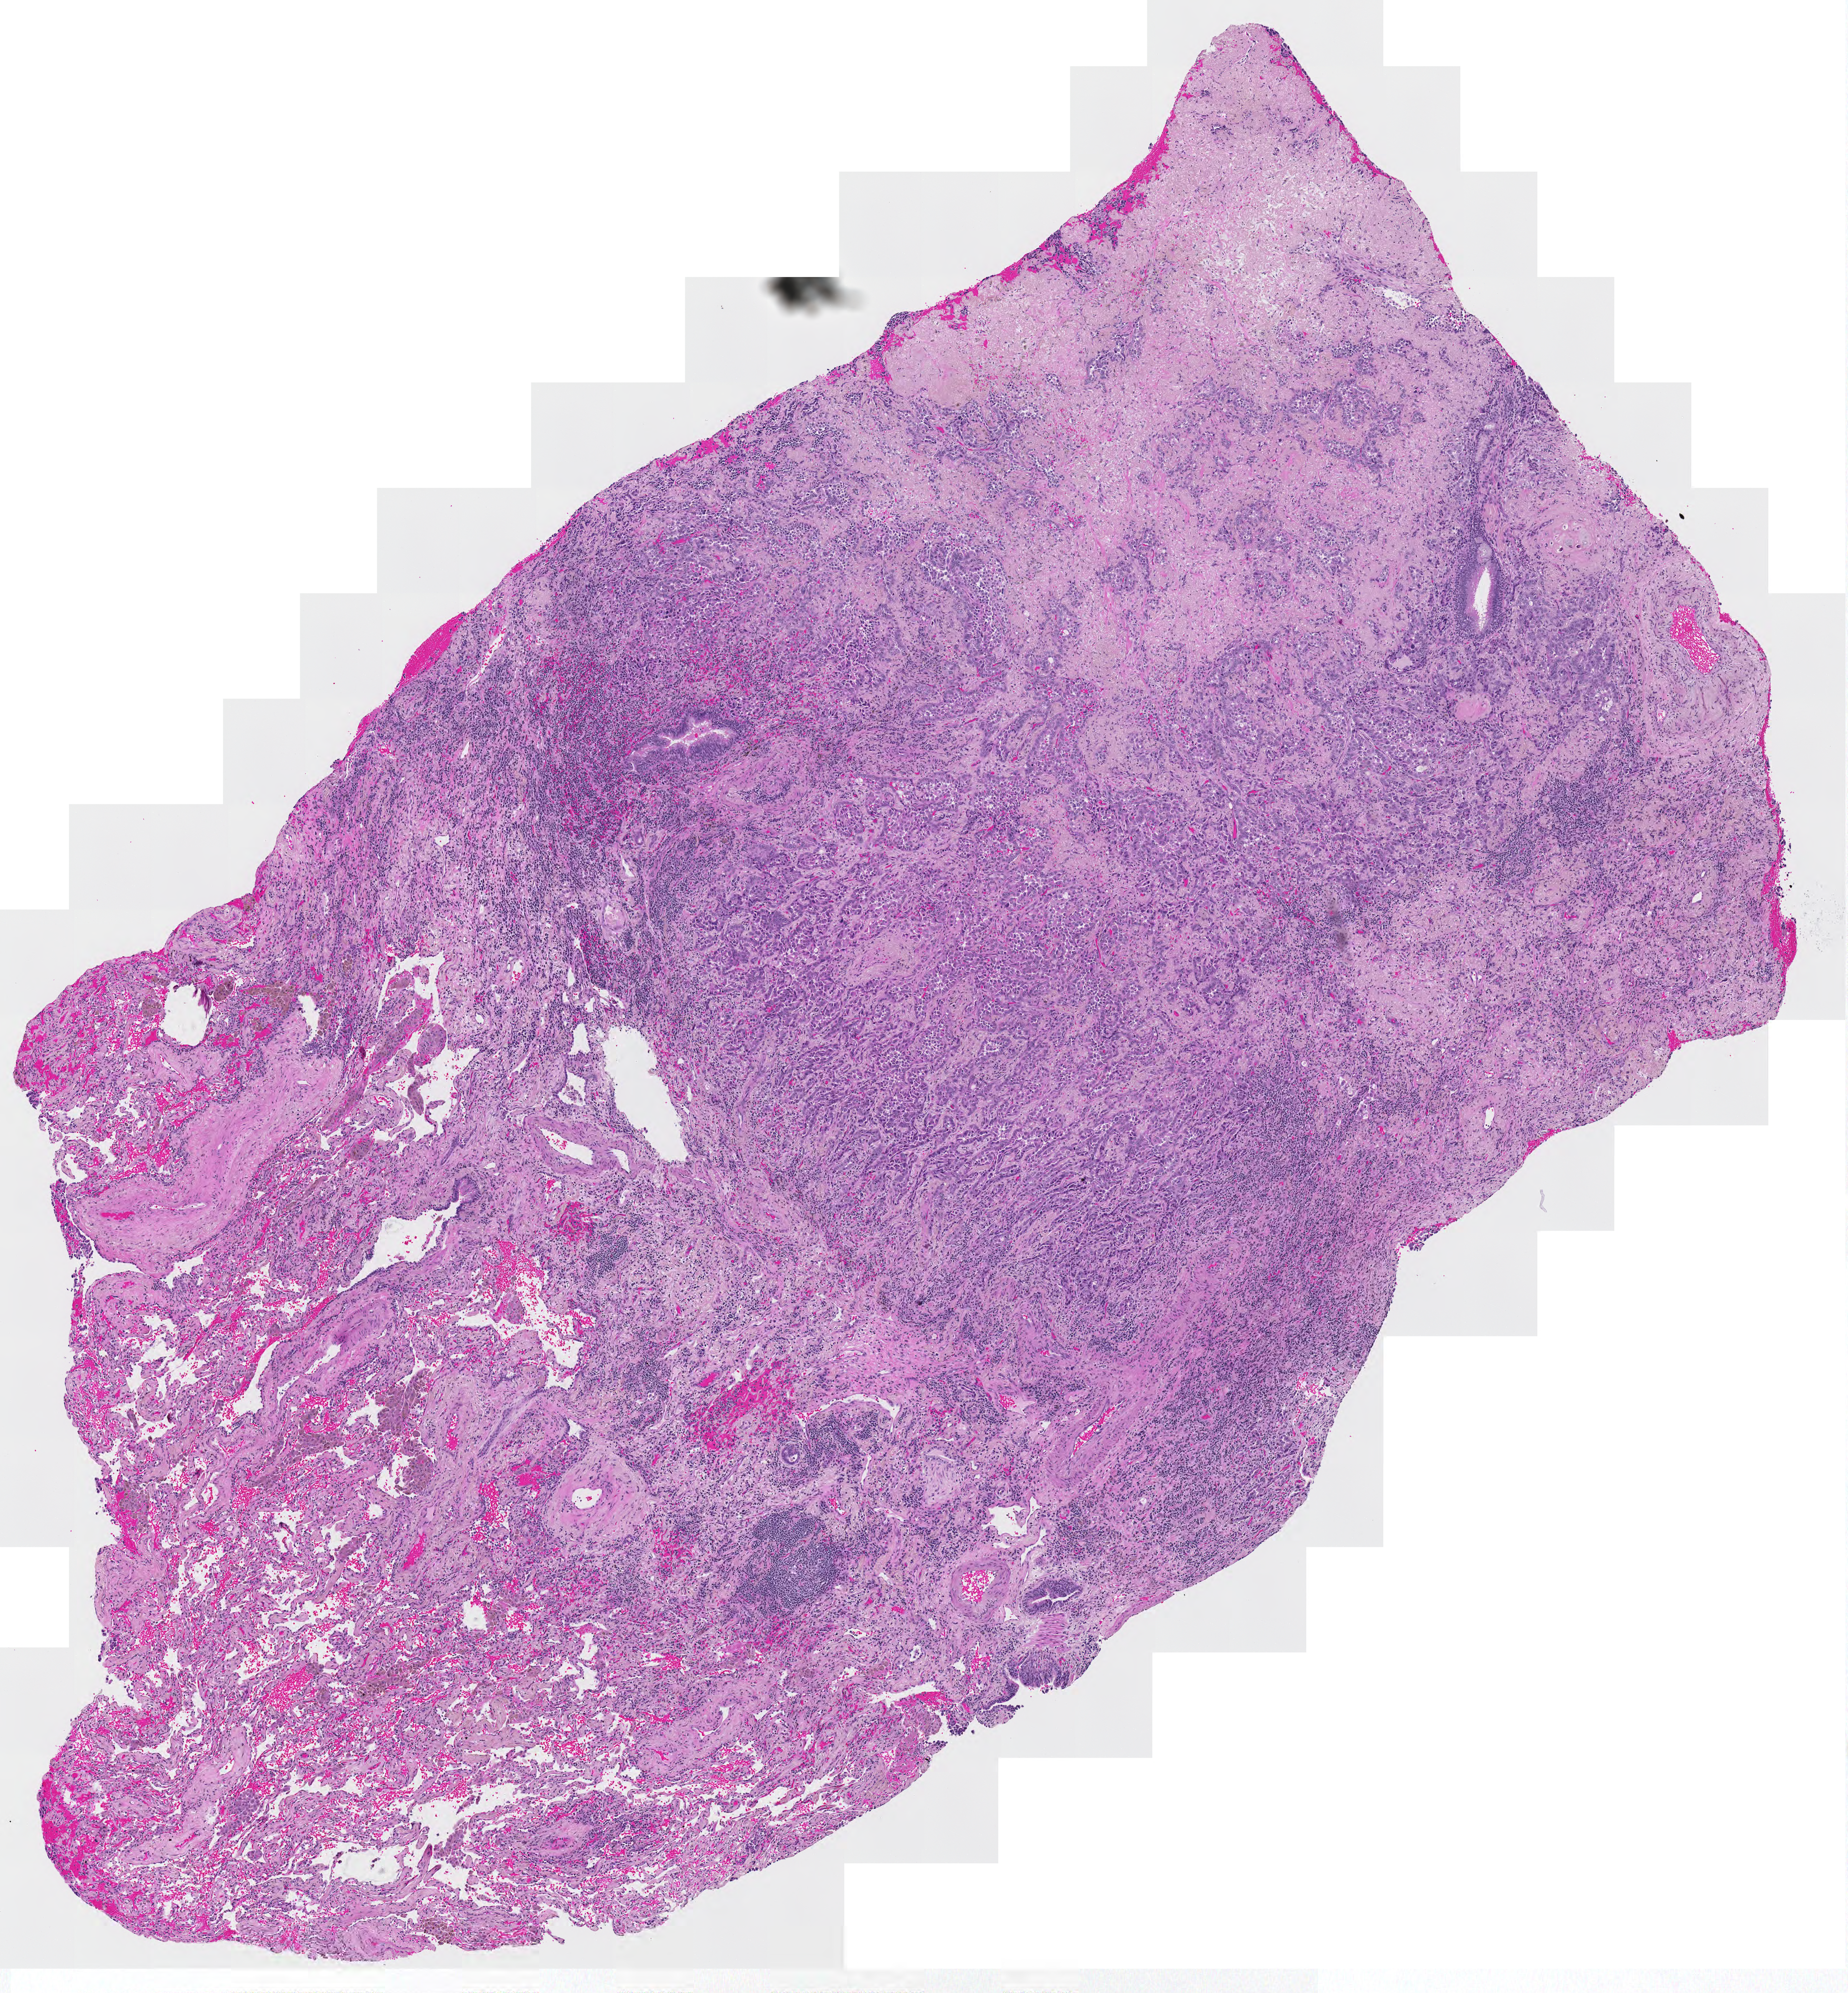
Digitized Hematoxylin and eosin (H&E) stained tissue section (whole slide) — shown as a low-resolution overview of the whole scanned area (about 7.4 x 8.0 mm). Tumour tissue sample, lung. Female, 68 y/o. Histologic grade: G2 (moderately differentiated).
Primary tumour site (as recorded): right upper lobe. Histologic diagnosis: Adenocarcinoma, NOS. AJCC pathologic stage: IA.